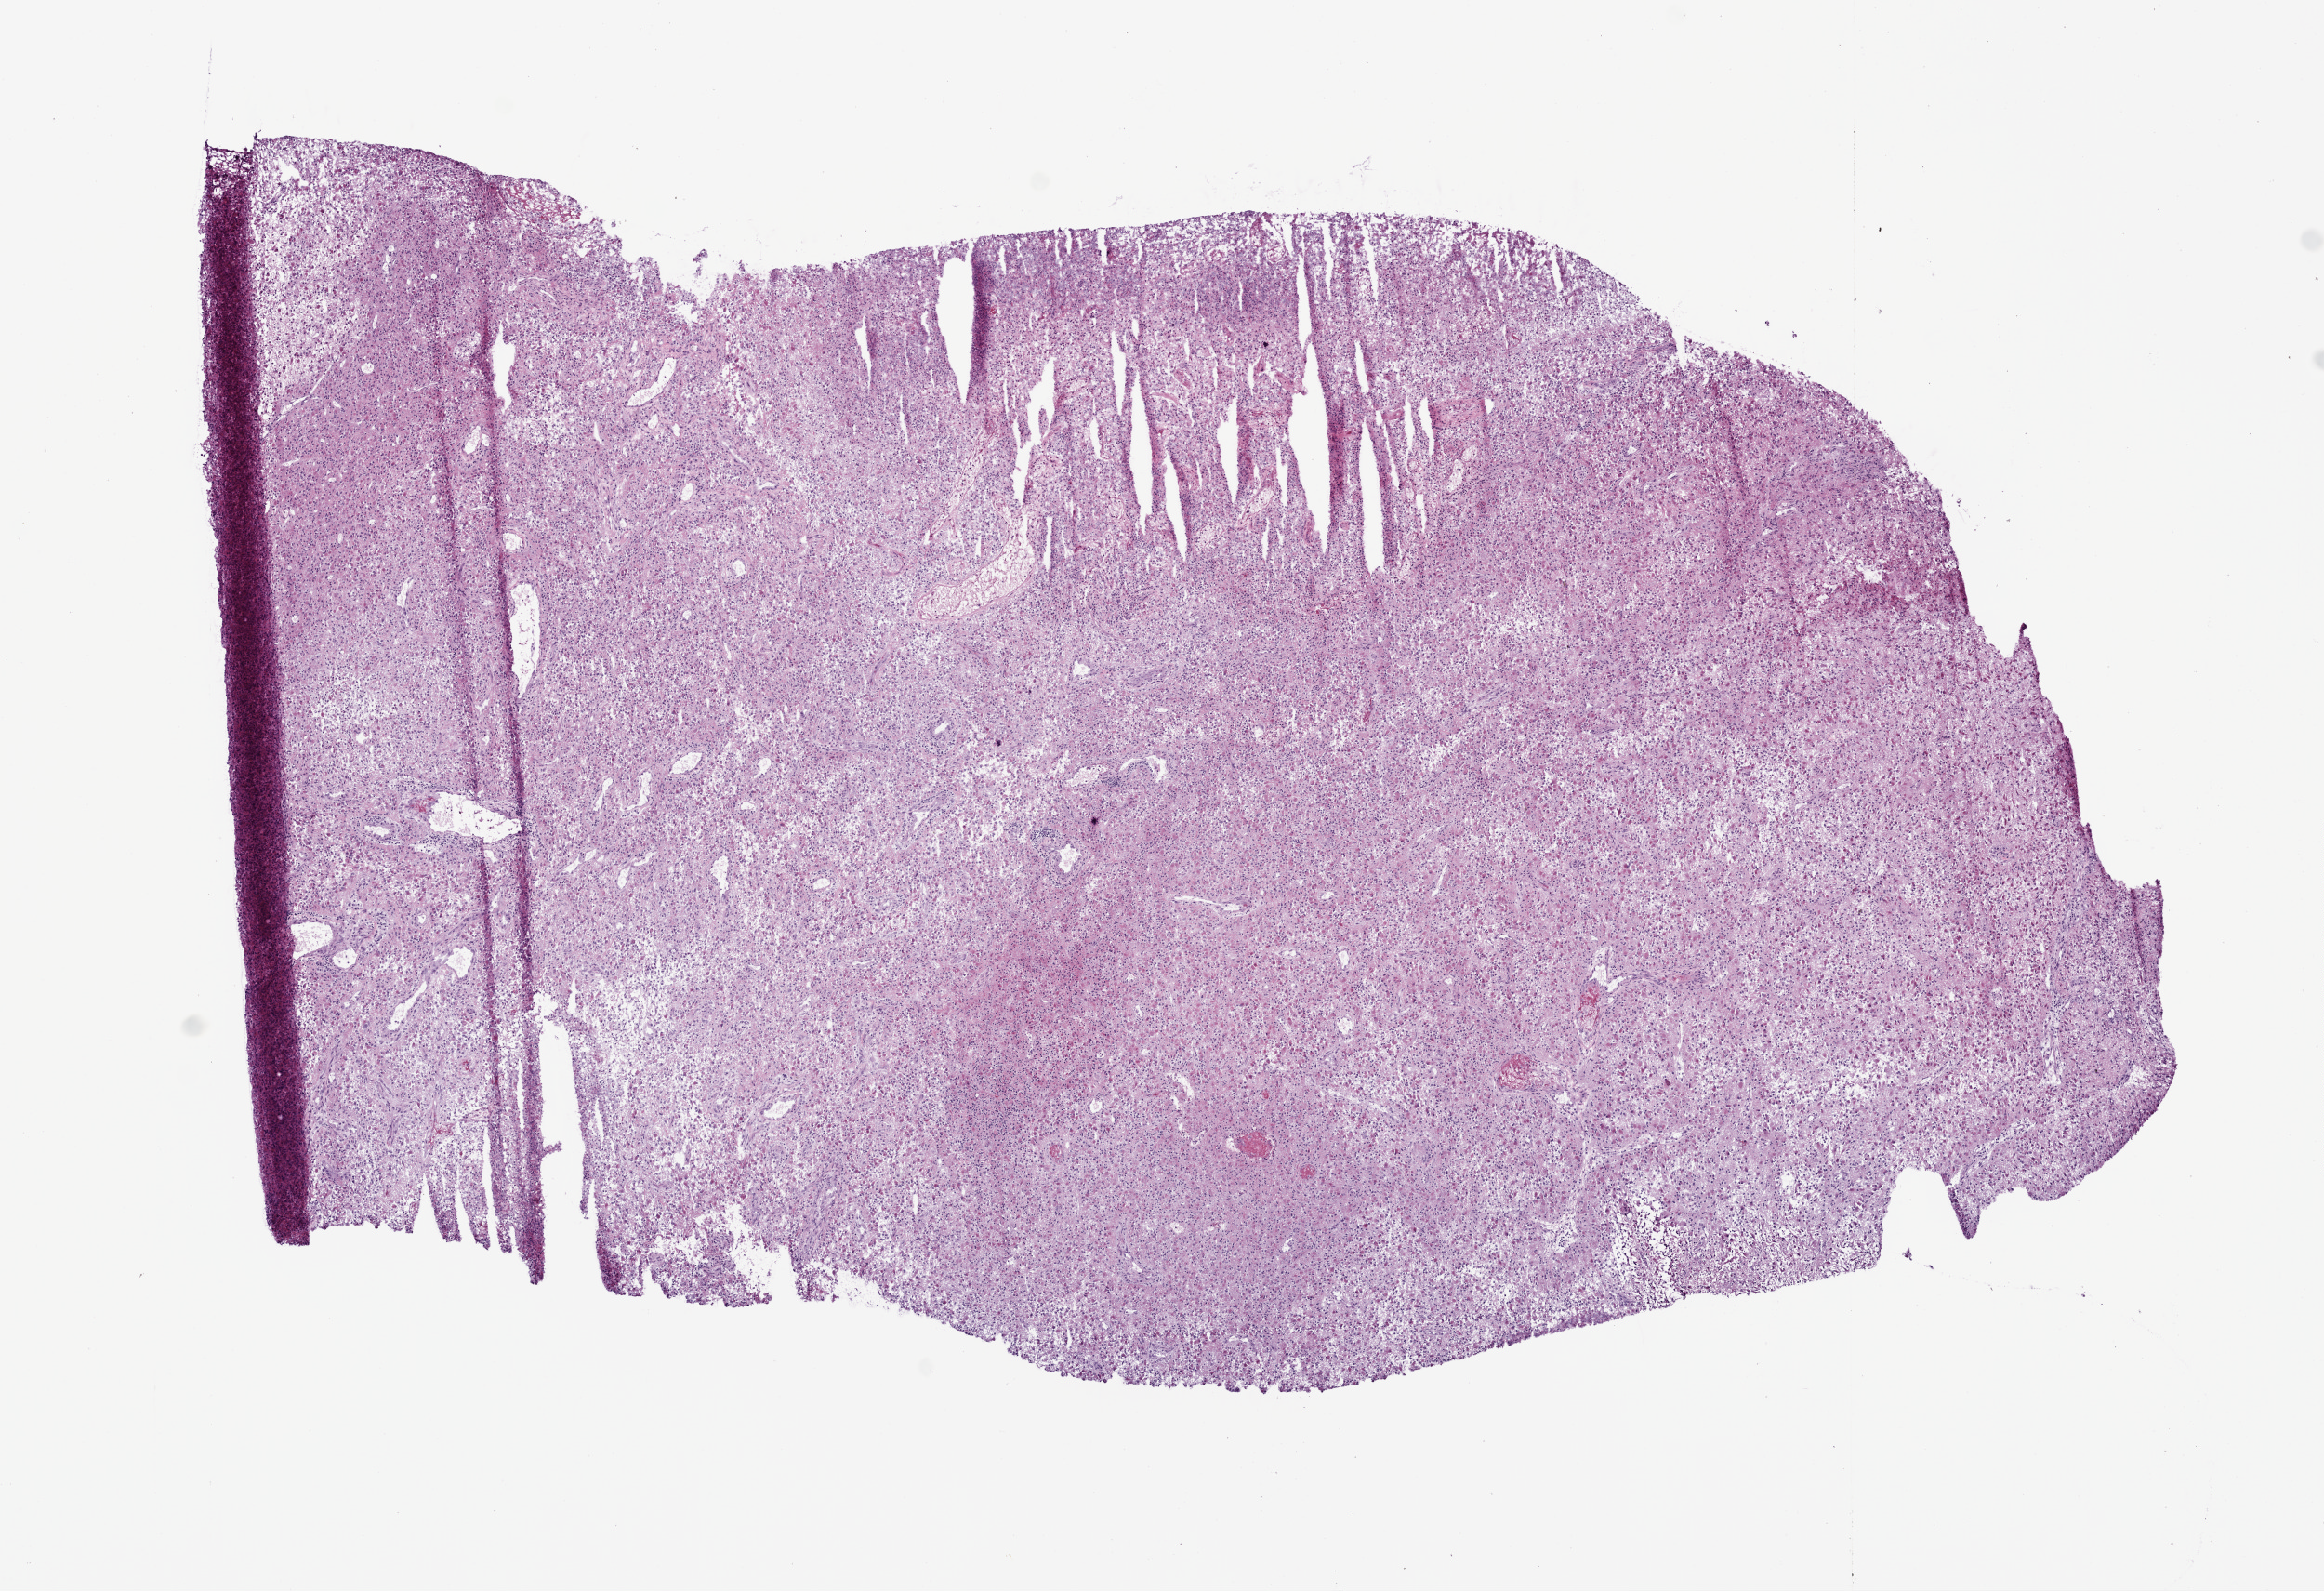
Digitized Hematoxylin and eosin (H&E) stained tissue section (whole slide) — a low-resolution overview of the entire scanned area, about 10.0 x 6.9 mm, frozen section from the bottom of the tissue portion, primary tumour sample from the brain. Male, age 72 years at initial diagnosis. Pathologist review of this section (percent, as recorded): tumour cells 99%, tumour nuclei 80%, normal cells 0%, stromal cells 0%, necrosis 1%.
Diagnosis: Glioblastoma.